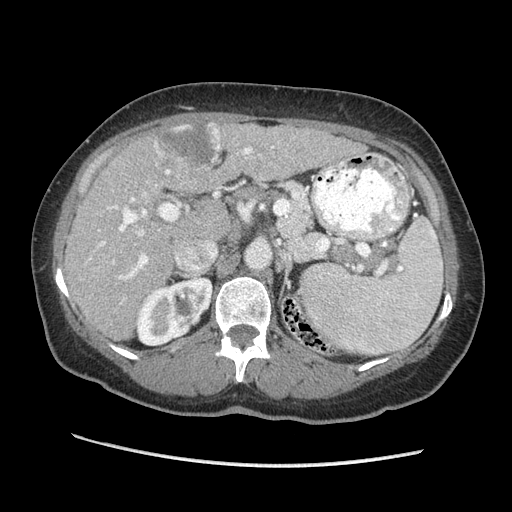
Contrast-enhanced abdominal CT (liver protocol), one axial slice. Position 129 of 170 along the scan axis. 140 kVp. Soft-tissue window (W 400 / L 40 HU). 2.5 mm slice thickness. 512 × 512 image matrix, field of view 360 × 360 mm. From the clinical record (not read from this slice): diagnosis: hepatocellular carcinoma (patient treated with transarterial chemoembolisation; whether this scan precedes or follows treatment is not stated here); TNM stage (as recorded): Stage-II; Child-Pugh class: A; tumour differentiation: no biopsy; tumour size: 4 cm.
Structures marked on this image (semi-automatically segmented with operator editing):
- liver parenchyma outside the tumour (the mass and vessels are separate outlines, so this box may not span the whole liver): bounding box [x1, y1, x2, y2] px = [64, 121, 365, 340]
- mass: [156, 120, 221, 173]
- liver vessels: [89, 144, 274, 280]